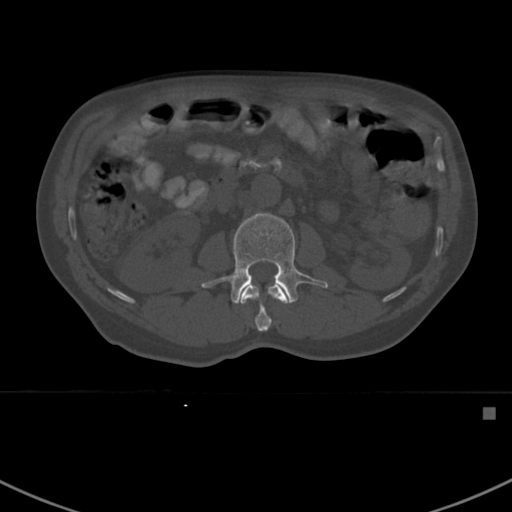
CT including the spine, one axial slice; slice 293 of 412 in the series (ordered by position); 120 kVp; bone window (W 1800 / L 400 HU); 512 × 512 image matrix, field of view 358 × 358 mm. Patient: male, 59 years. From the clinical record (not read from this slice): primary cancer: prostate.
Structures marked on this image (semi-automatic segmentation, software-assisted and operator-edited):
- L1 vertebra: bounding box <240,285,288,332> (left, top, right, bottom; pixels)
- L2 vertebra: <201,213,328,304>